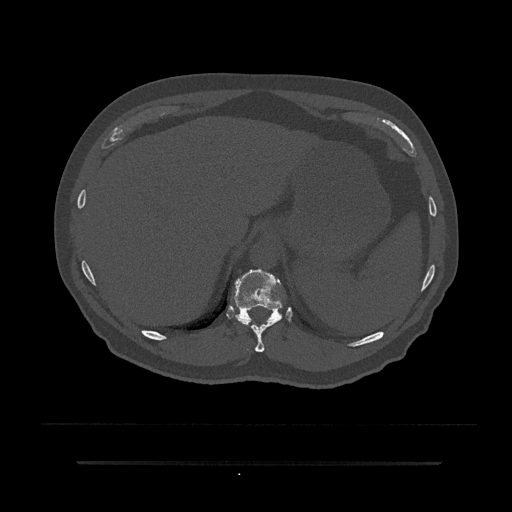
CT including the spine, one axial slice; slice 297 of 797 in the series (ordered by position); reconstruction kernel Br40s/3; 120 kVp; bone window (W 1800 / L 400 HU); 512 × 512 image matrix. Patient: male, 59 years. From the clinical record (not read from this slice): primary cancer: bile ducts.
Annotated regions visible in this slice (semi-automatic segmentation, software-assisted and operator-edited):
- T10 vertebra: bounding box [x1, y1, x2, y2] px = [236, 307, 282, 352]
- T11 vertebra: [229, 269, 289, 323]